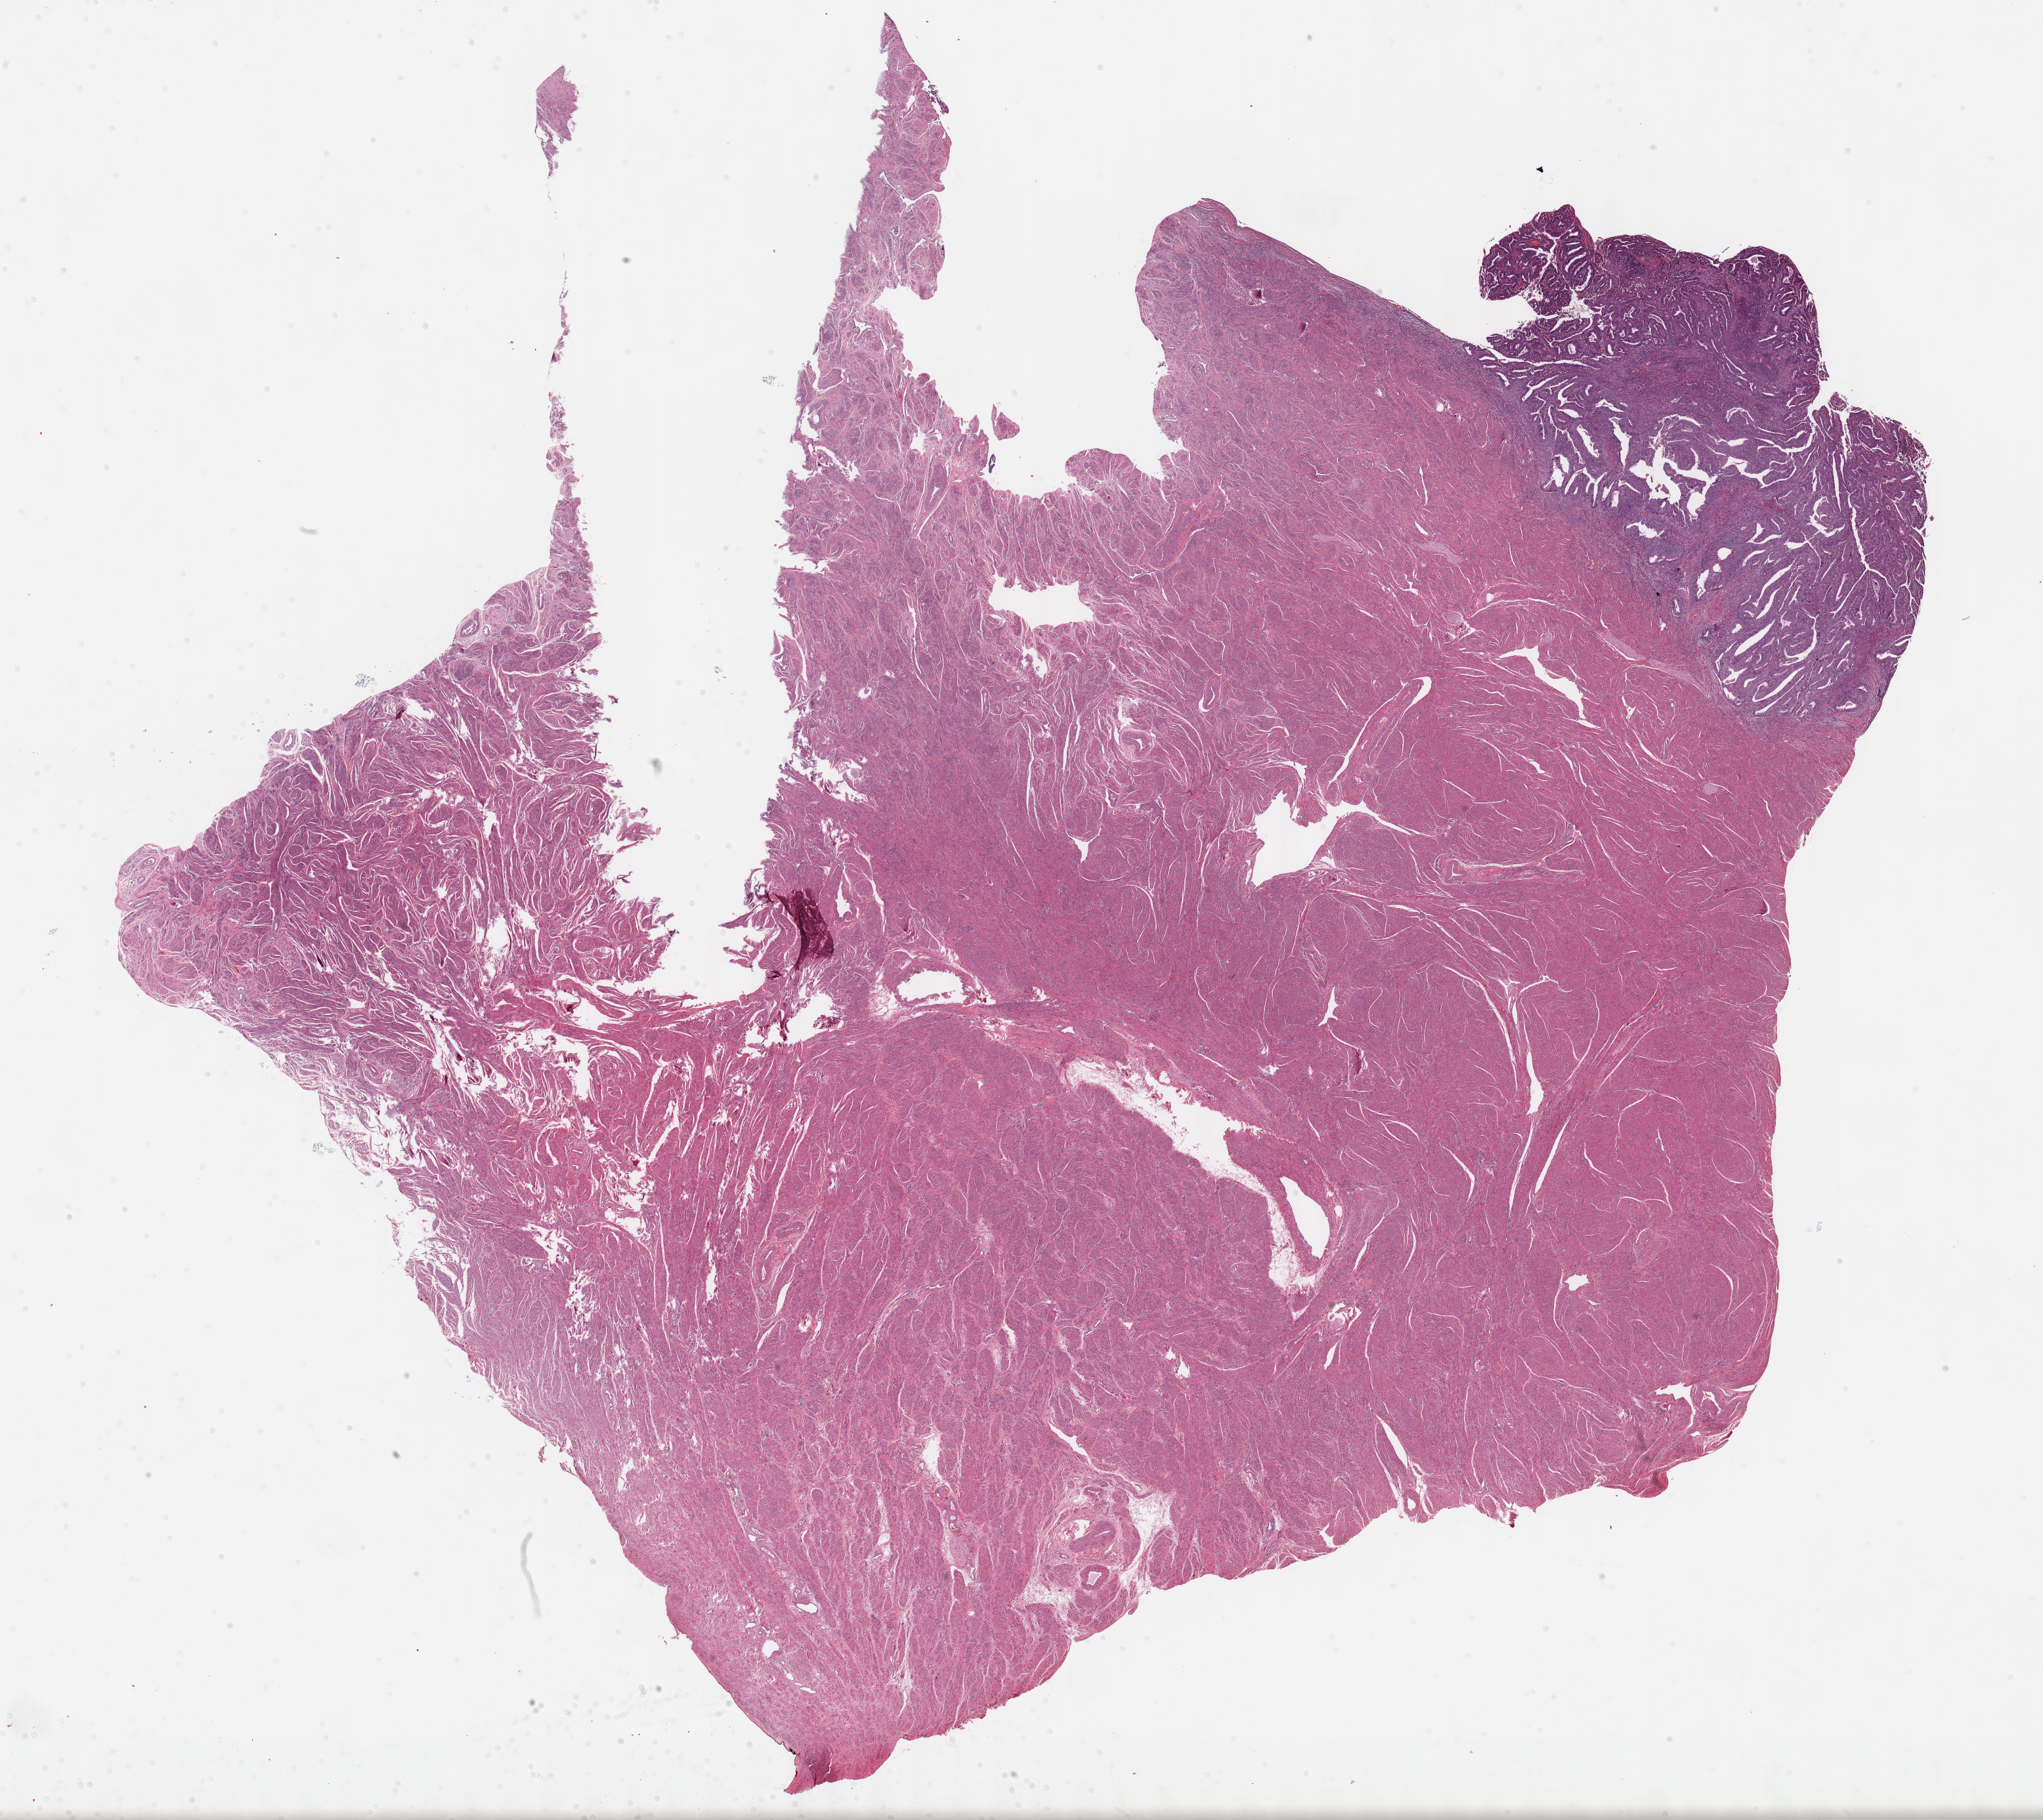
Digitized H&E tissue section (whole slide) — shown as a low-resolution overview of the whole scanned area (about 25.2 x 22.4 mm), formalin-fixed paraffin-embedded (FFPE) diagnostic section, primary tumour sample from the uterus. Female patient; age at initial diagnosis 57 years. Histologic grade: G1 (well differentiated).
• diagnosis: Endometrioid adenocarcinoma, NOS (isthmus uteri)
• FIGO stage: II